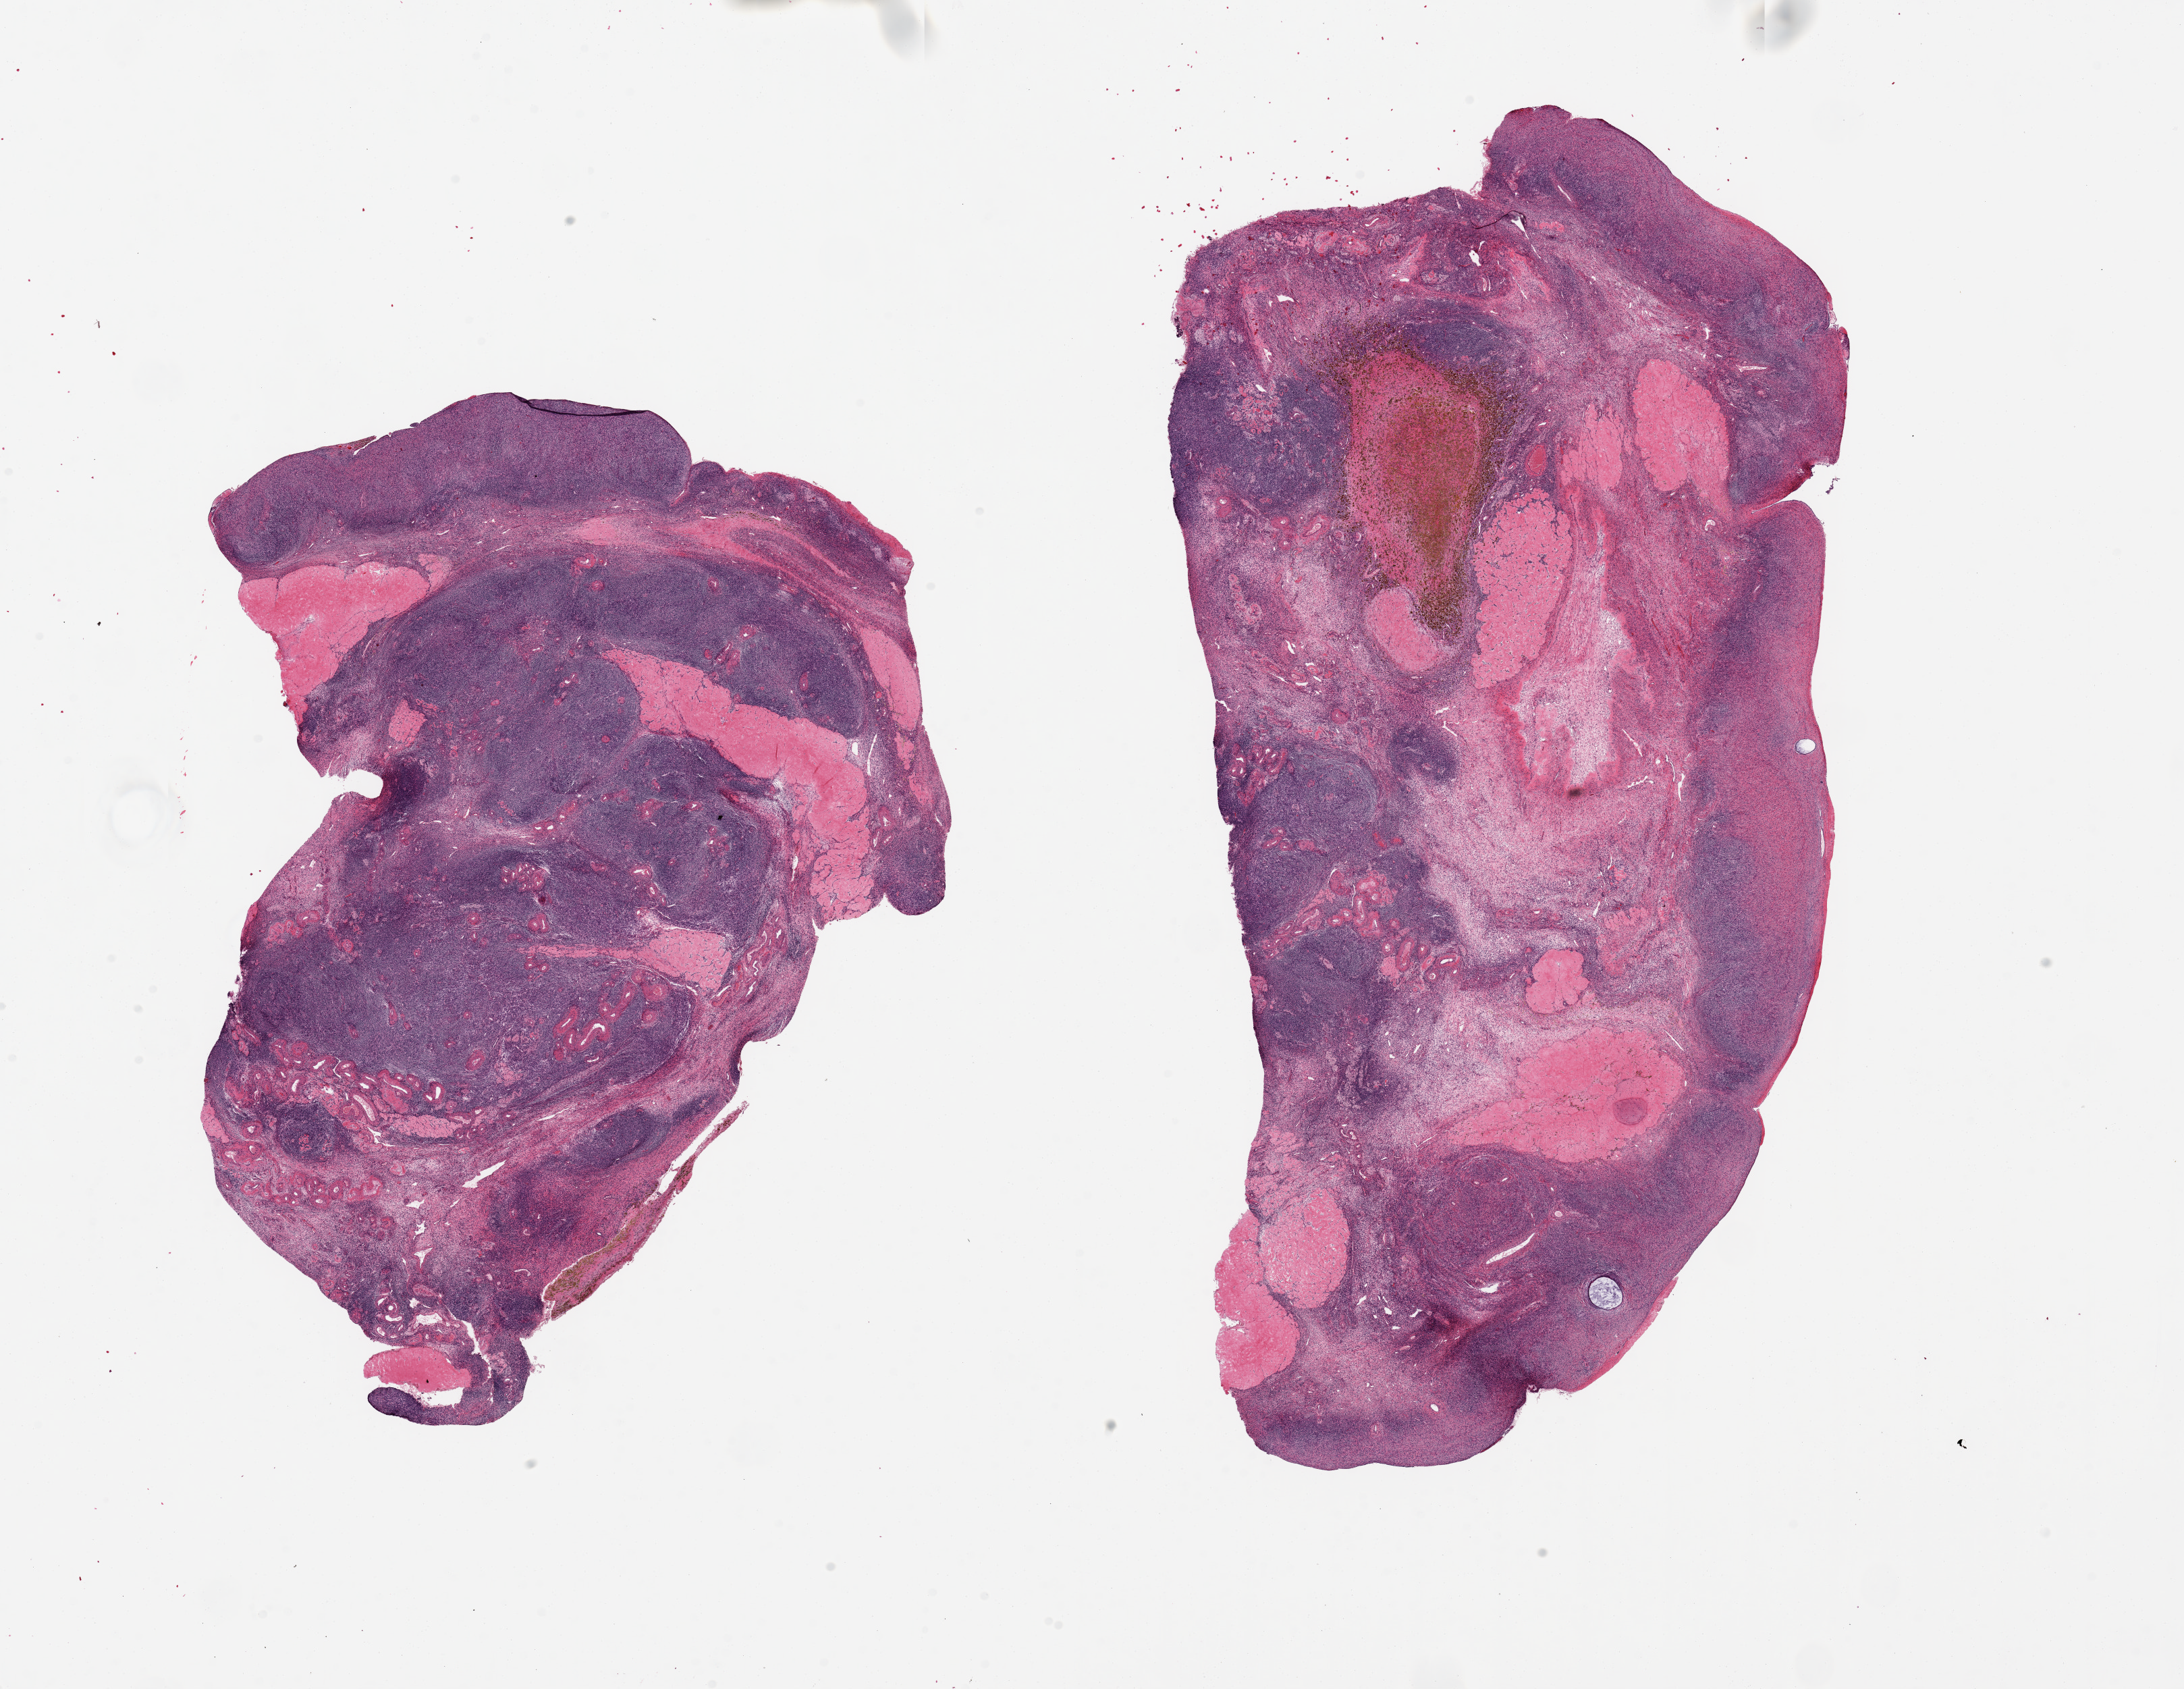
Digitized H&E-stained section — a low-resolution overview of the entire scanned area, about 25.6 x 19.8 mm (slide scanned at 20x). PAXgene-fixed paraffin-embedded (PFPE) section. Target tissue: ovary. Tissue donor sample. Donor: female.
Review note (as recorded): 2 pieces, 12x9 & 16x8mm; ~30% corpora albicantia.